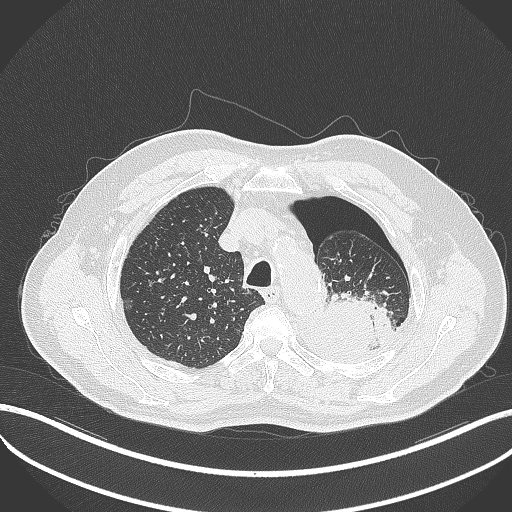
Chest CT, one axial slice; slice 398 of 464 in the series (ordered by position); lung window (W 1500 / L -600 HU); 1 mm slice thickness; 512 × 512 image matrix, field of view 400 × 400 mm. Patient: male, 76 years. From the clinical record (not read from this slice): clinical TNM (as recorded): T3 N0 M1b.
Structures marked on this image (rectangle marked by the reading radiologist):
- lung tumour (recorded histology: adenocarcinoma): bounding box [x1, y1, x2, y2] px = [315, 294, 396, 358]